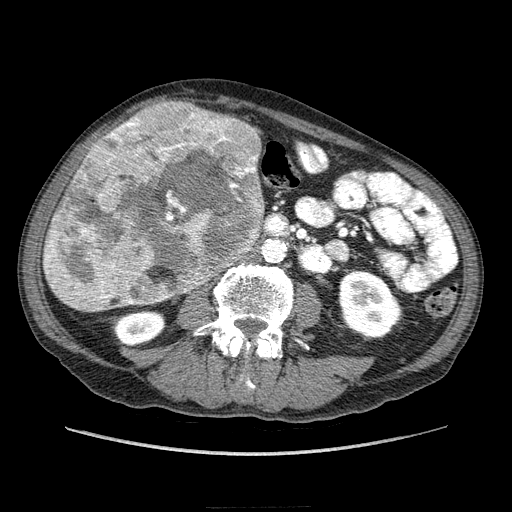
Contrast-enhanced abdominal CT (liver protocol), one axial slice; 100 kVp; soft-tissue window (W 400 / L 40 HU); 2.5 mm slice thickness; 512 × 512 image matrix, field of view 380 × 380 mm. Case-level facts recorded for this patient, not image findings: diagnosis: hepatocellular carcinoma (patient treated with transarterial chemoembolisation; whether this scan precedes or follows treatment is not stated here); TNM stage (as recorded): Stage-IIIA; Child-Pugh class: A; tumour differentiation: well differentiated; tumour nodularity: multinodular.
Outlined on this slice (semi-automatically segmented with operator editing):
- liver parenchyma outside the tumour (the mass and vessels are separate outlines, so this box may not span the whole liver): bounding box <44,132,112,277> (left, top, right, bottom; pixels)
- mass: <44,101,266,311>